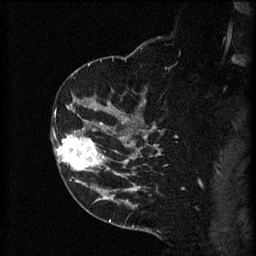
Breast MRI (dynamic contrast-enhanced), one sagittal slice. Position 40 of 60 along the scan axis. 3 images stored at this slice position (order not interpretable as contrast timing). 1.5 T. TE 4.2 ms, TR 8.2 ms. 256 × 256 image matrix. Patient: female, 49 years.
Annotated regions visible in this slice (semi-automatic segmentation, software-assisted and operator-edited):
- analysis volume of interest (the breast-tissue region the enhancement analysis was run in; not a lesion): bounding box (x1, y1, x2, y2) in pixels: (51, 126, 105, 177)
- tumour enhancement mask (voxels above the 70 % enhancement threshold inside the analysis volume of interest): (54, 134, 105, 171)